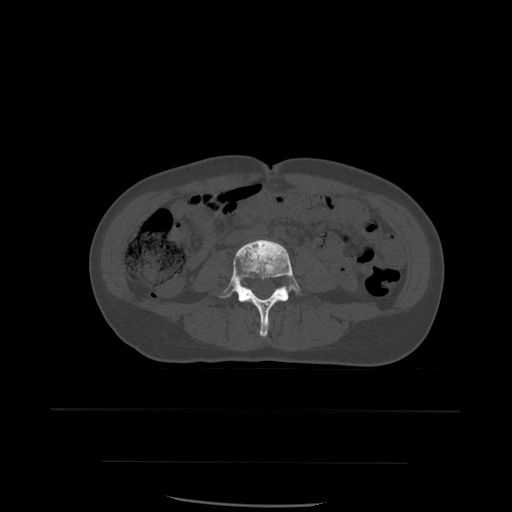
CT including the spine, one axial slice. Position 172 of 574 along the scan axis. Bone window (W 1800 / L 400 HU). 512 × 512 image matrix, field of view 392 × 392 mm. Patient age 48 years. From the clinical record (not read from this slice): primary cancer: lung; vertebrae with lytic lesions (as recorded): T11.
Annotated regions visible in this slice (semi-automatic segmentation, software-assisted and operator-edited):
- L4 vertebra: box from (x=218, y=239) to (x=302, y=337) px